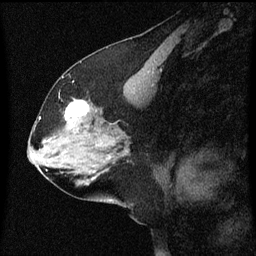
Breast MRI (dynamic contrast-enhanced), one sagittal slice. Position 30 of 60 along the scan axis. Dynamic contrast-enhanced series, image 2 of 3 at this slice position (ordered by acquisition). 1.5 T. TE 4.2 ms, TR 8 ms. 2 mm slice thickness. 256 × 256 image matrix, field of view 200 × 200 mm. Female patient, age 58 years.
Annotated regions visible in this slice (semi-automatic segmentation, software-assisted and operator-edited):
- analysis volume of interest (the breast-tissue region the enhancement analysis was run in; not a lesion): bounding box <56,100,95,137> (left, top, right, bottom; pixels)
- tumour enhancement mask (voxels above the 70 % enhancement threshold inside the analysis volume of interest): <66,102,89,125>